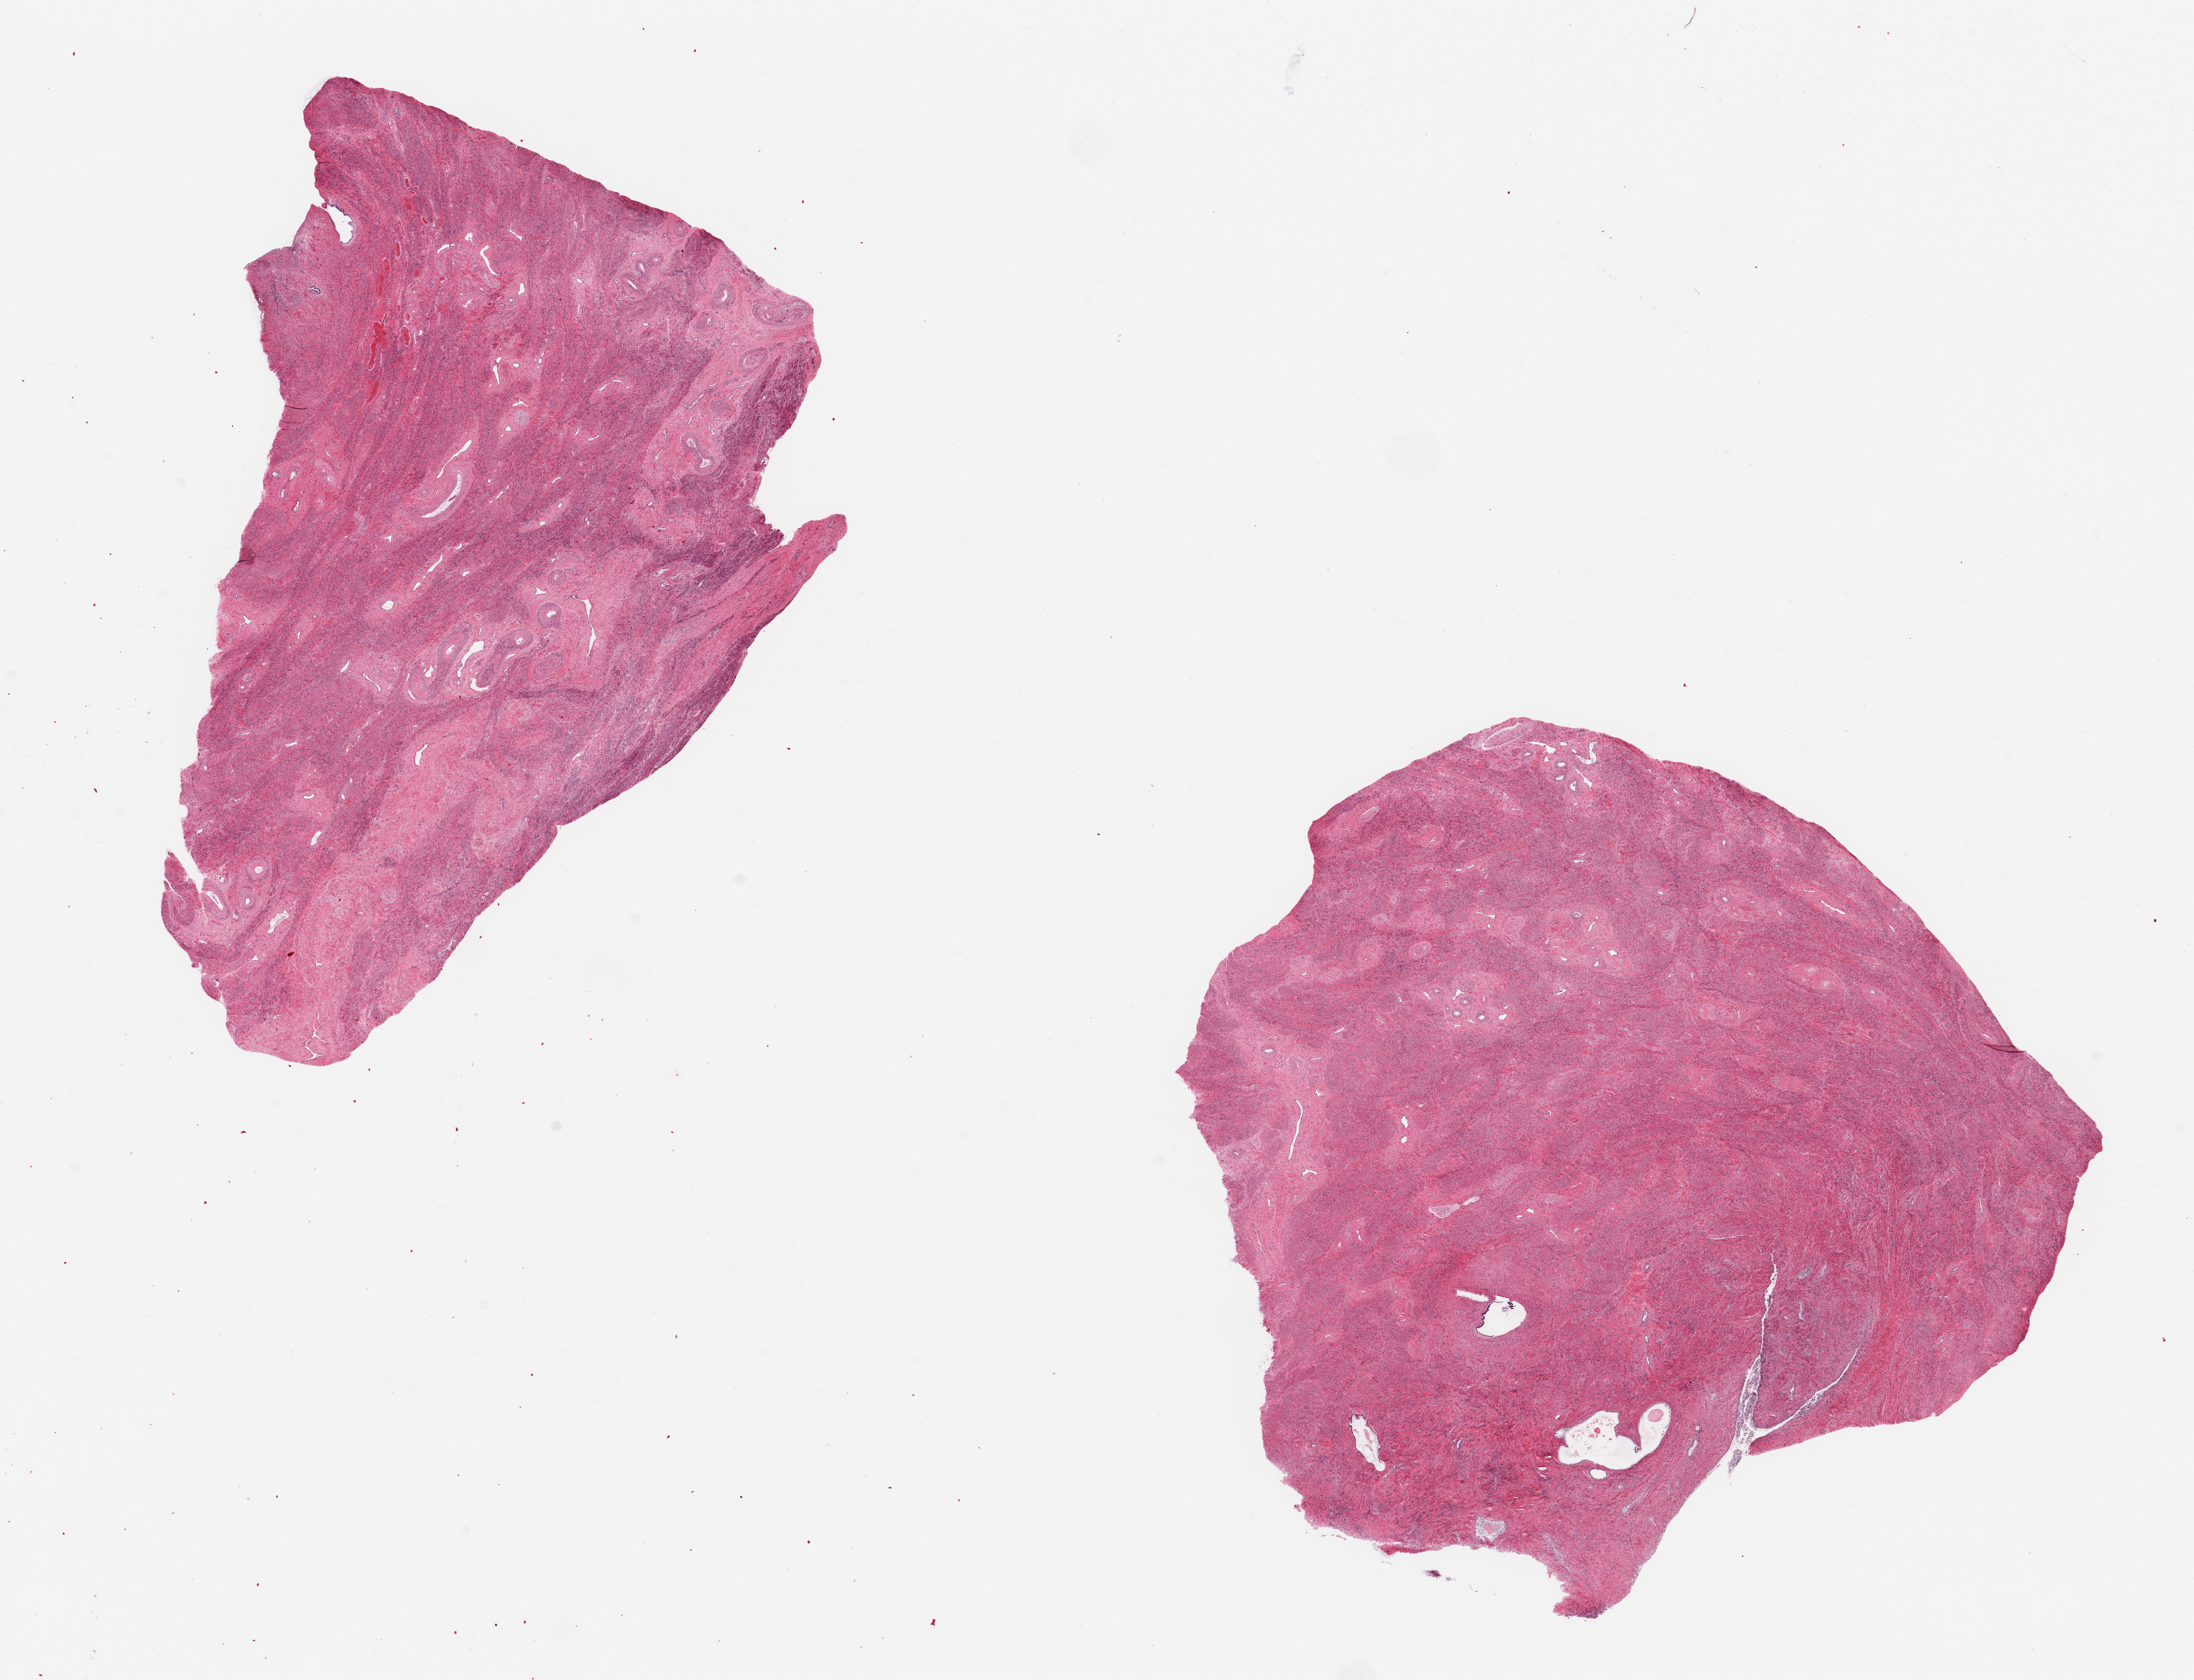
Whole-slide image, hematoxylin and eosin (H&E) stain, whole scanned area (about 24.6 x 18.8 mm, acquisition: 20x scan) shown as a low-resolution overview; PAXgene-fixed paraffin-embedded (PFPE) section; sampled site (target tissue): uterus; tissue donor sample. Donor: female.
Review note (as recorded): 2 pieces, degnerating glandular elements, probably autolyzed adenomyosis.